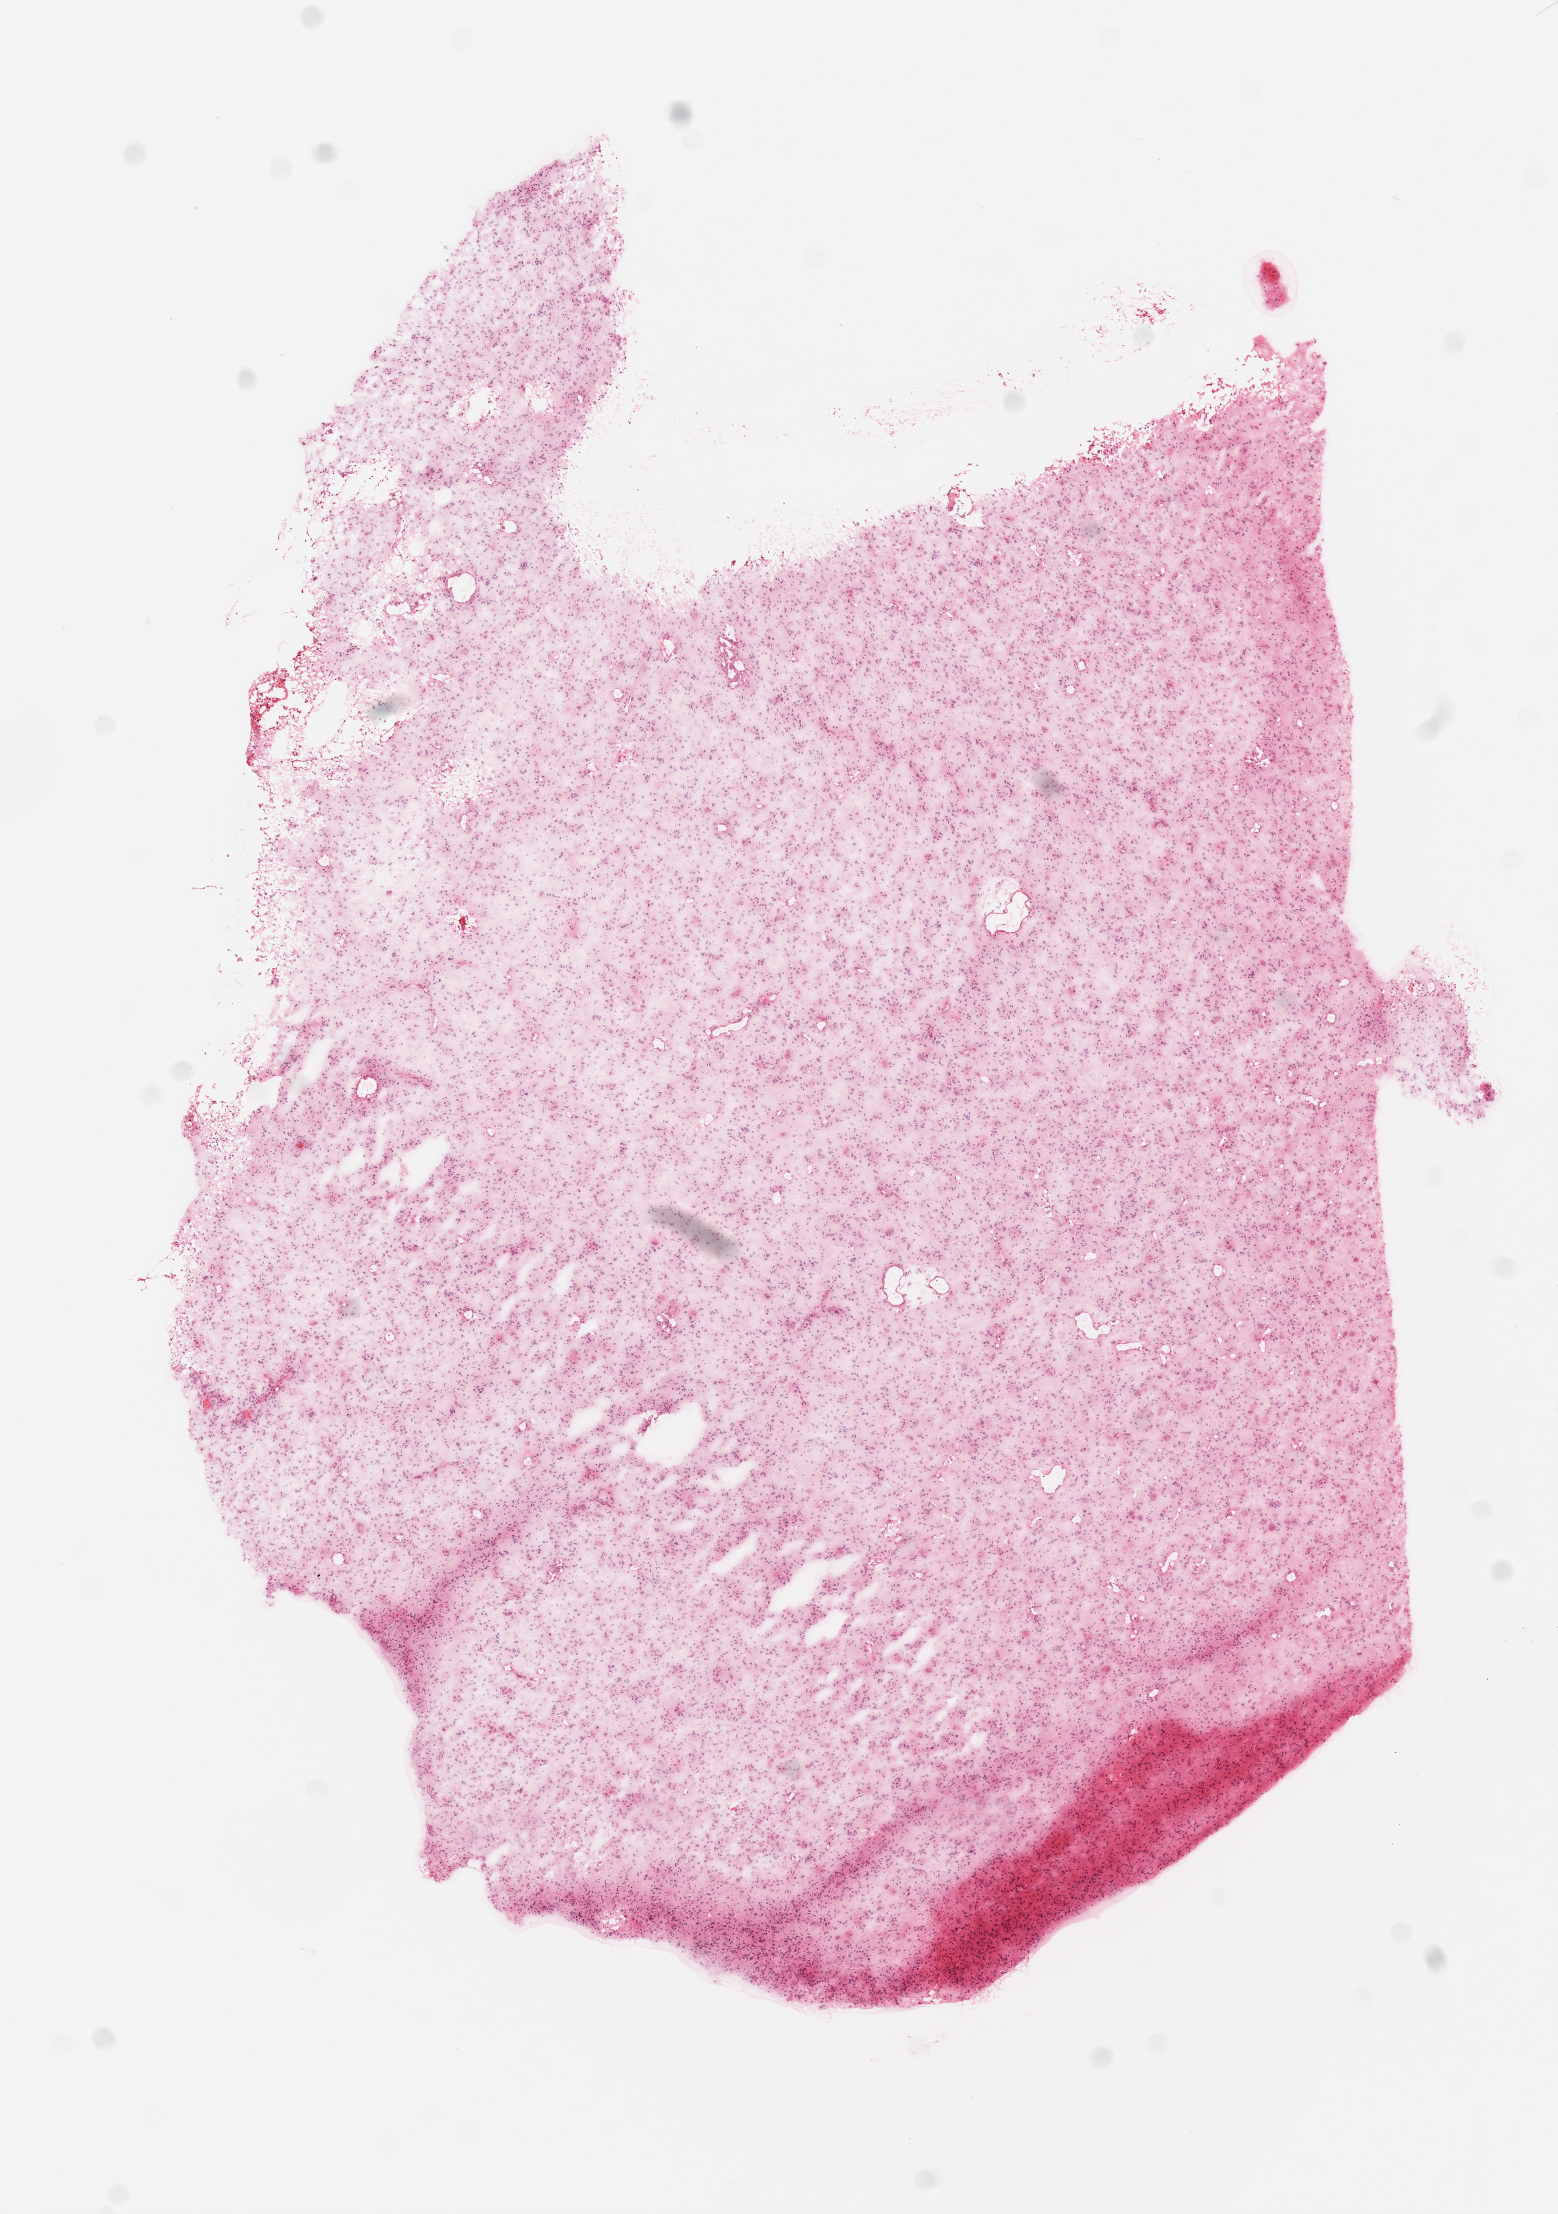
Digitized H&E-stained tissue section (whole slide), whole scanned area (about 6.3 x 8.9 mm, slide scanned at 20x) shown as a low-resolution overview; frozen section from the bottom of the tissue portion; brain, primary tumour sample. Male, age 50 years at initial diagnosis. Slide review estimates, as recorded: tumour cells 80%, tumour nuclei 80%, normal cells 0%, stromal cells 20%, necrosis 0%.
• histologic diagnosis: Glioblastoma